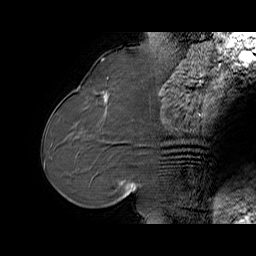
Breast MRI (dynamic contrast-enhanced), one sagittal slice; slice 26 of 65 in the series (ordered by position); dynamic contrast-enhanced series, time point 2 of 6 at this slice position (early post-contrast); 1.5 T; TE 5.7 ms, TR 32.9 ms; 4 mm slice thickness; 256 × 256 image matrix. Female patient. From the clinical record (not read from this slice): setting: breast cancer imaged before/during neoadjuvant chemotherapy; receptor status: HER2-positive.
Outlined on this slice (semi-automatically segmented with operator editing):
- analysis volume of interest (the breast-tissue region the enhancement analysis was run in; not a lesion): bounding box (x1, y1, x2, y2) in pixels: (76, 77, 125, 128)
- tumour enhancement mask (voxels above the 100 % enhancement threshold inside the analysis volume of interest): (103, 92, 107, 102)